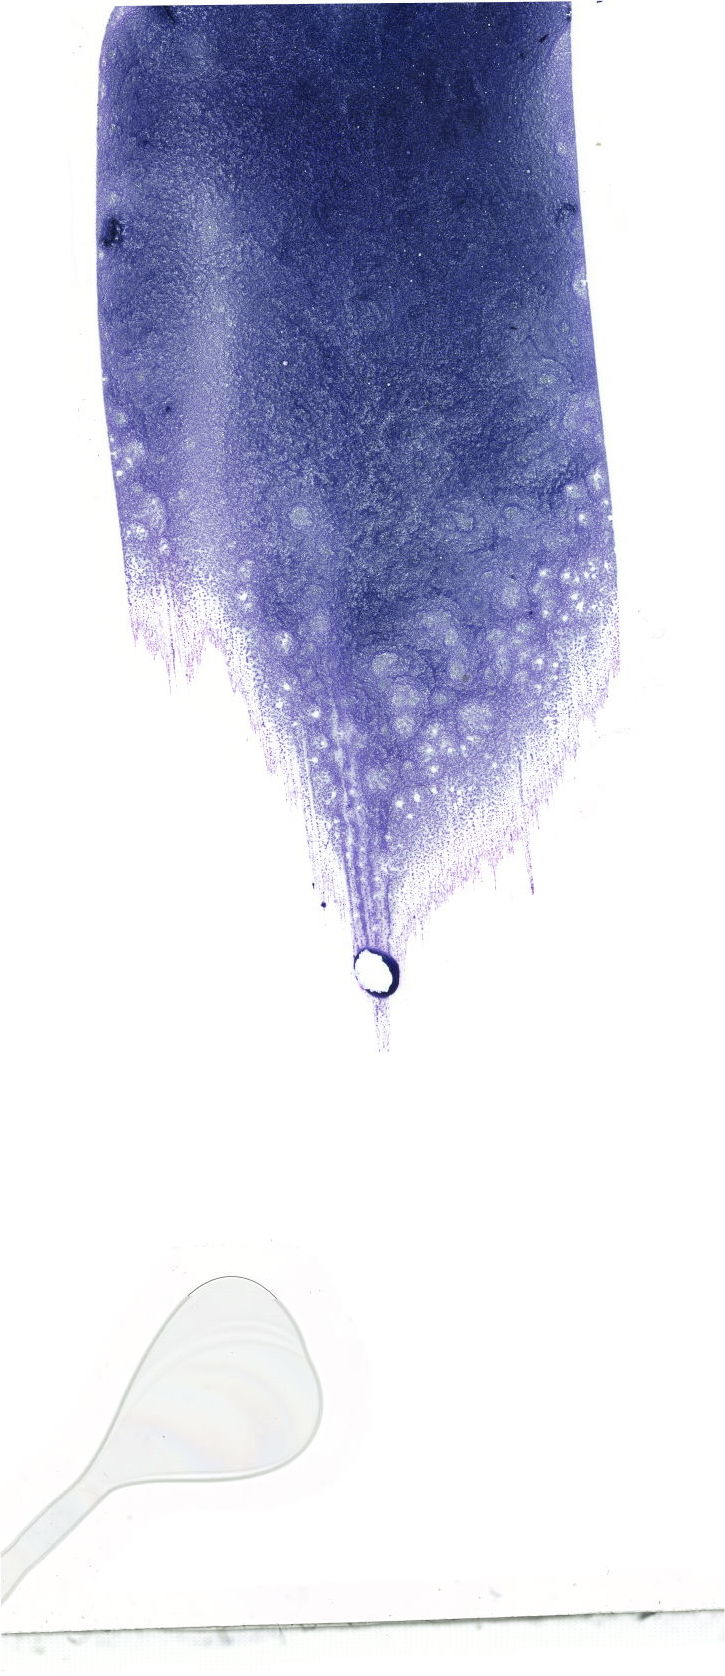
Whole-slide image of a May-Grünwald-Giemsa (MGG)-stained bone marrow aspirate smear, low-resolution overview of the scanned area, about 20.6 x 47.5 mm. Patient sex: female.
Diagnosis: Chronic Phase Chronic Myeloid Leukemia, BCR-ABL1 Positive.